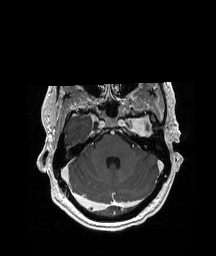
Brain MRI from a brain-tumour surgery series, one axial slice. Position 143 of 208 along the scan axis. T1-weighted post-contrast. 1 mm slice thickness. 216 × 256 image matrix, field of view 228 × 270 mm. Case-level facts recorded for this patient, not image findings: histopathology: Glioblastoma; WHO grade: 4; IDH mutation: no.
Structures marked on this image (manually delineated by an expert):
- previous resection cavity: bounding box [x1, y1, x2, y2] px = [147, 127, 151, 131]
- tumour: [123, 110, 158, 132]